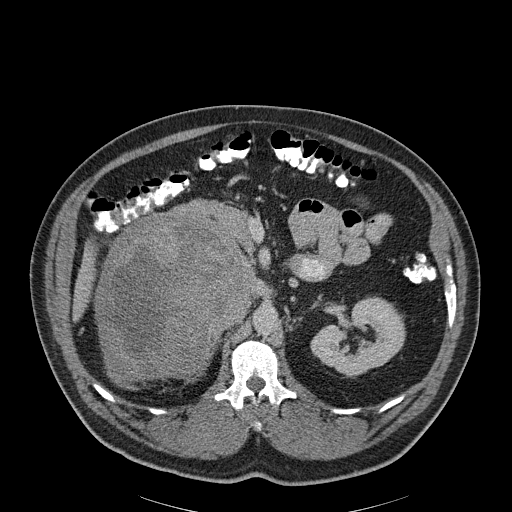
Contrast-enhanced abdominal CT, one axial slice. Position 123 of 186 along the scan axis. Soft-tissue window (W 400 / L 40 HU). 3 mm slice thickness. 512 × 512 image matrix. Male patient, age 56 years. From the clinical record (not read from this slice): diagnosis: adrenocortical carcinoma; tumour side: right adrenal; tumour size at pathology: 18 cm; Ki-67 index: 2 %; stage (as recorded): 3.
Structures marked on this image (semi-automatically segmented with operator editing):
- mass: bounding box (x1, y1, x2, y2) in pixels: (97, 215, 247, 382)